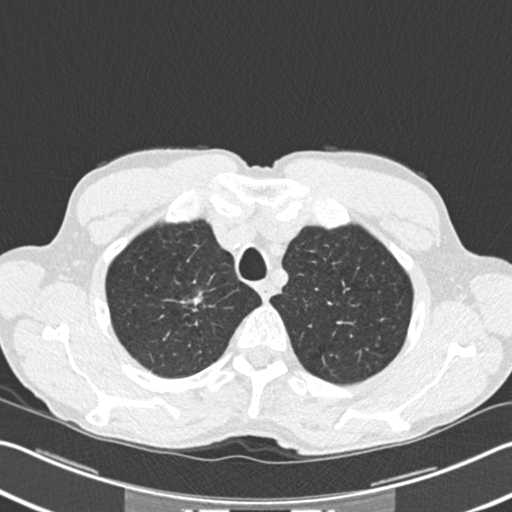
Low-dose screening chest CT, one axial slice; position 187 of 220 along the scan axis; lung window (W 1500 / L -600 HU); 2 mm slice thickness; 512 × 512 image matrix, field of view 342 × 342 mm.
Annotated regions visible in this slice (manually delineated by an expert):
- lesion 1 (tumor, upper lobe of right lung): box from (x=192, y=297) to (x=201, y=305) px